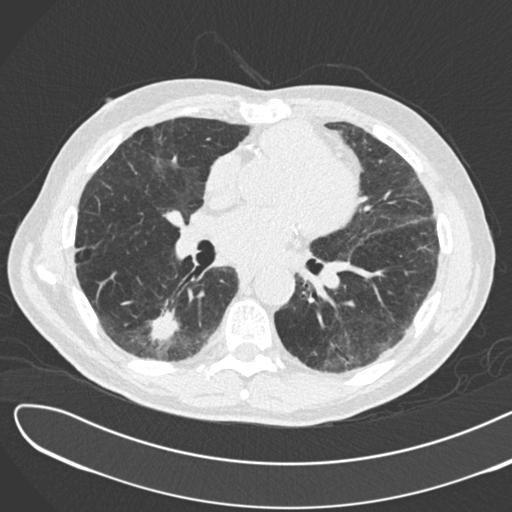
Chest CT (low-dose screening protocol), one axial image; second annual screen; lung window (W 1500 / L -600 HU); 2 mm slice thickness. Male, age 72 years at enrolment. Former smoker at enrolment.
- Expert reader's lesion annotation, bounding box (x1, y1, x2, y2) in pixels: (128, 290, 196, 354).
- The screening reader recorded 2 non-calcified nodules or masses ≥4 mm on this exam; which of them this box marks is not recorded.
- Official screen result: positive, change unspecified: nodule(s) >= 4 mm or enlarging nodule(s), mass(es), or other non-specific abnormalities suspicious for lung cancer.